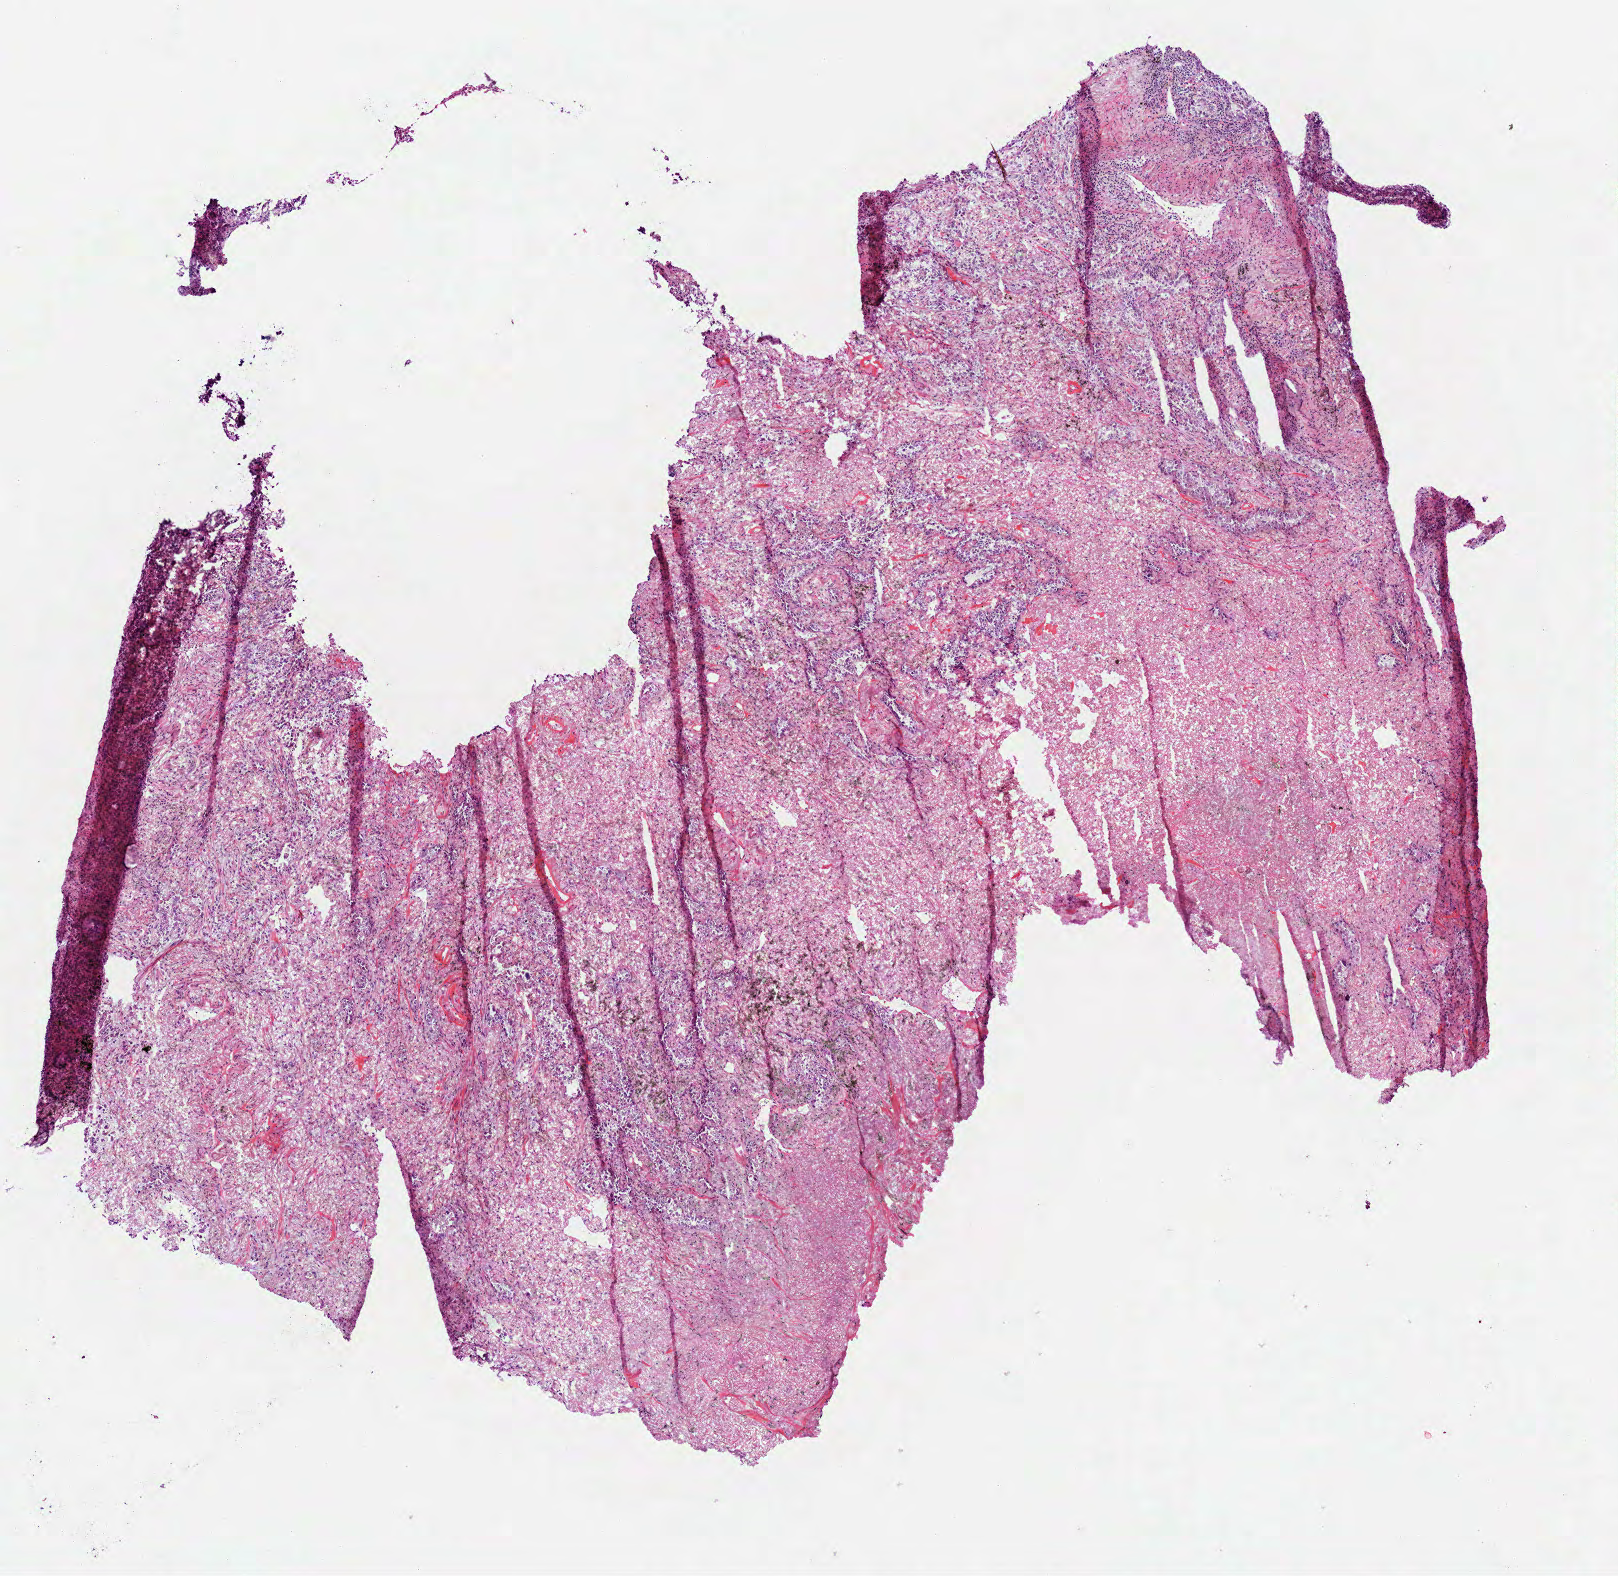
Hematoxylin and eosin (H&E) stained whole-slide image — a low-resolution overview of the entire scanned area, about 6.5 x 6.4 mm (acquisition: 40x scan), frozen section from the top of the tissue portion, sample: primary tumour, lung. Male, age 56 years at initial diagnosis.
Histologic diagnosis: Adenocarcinoma with mixed subtypes (upper lobe, lung).